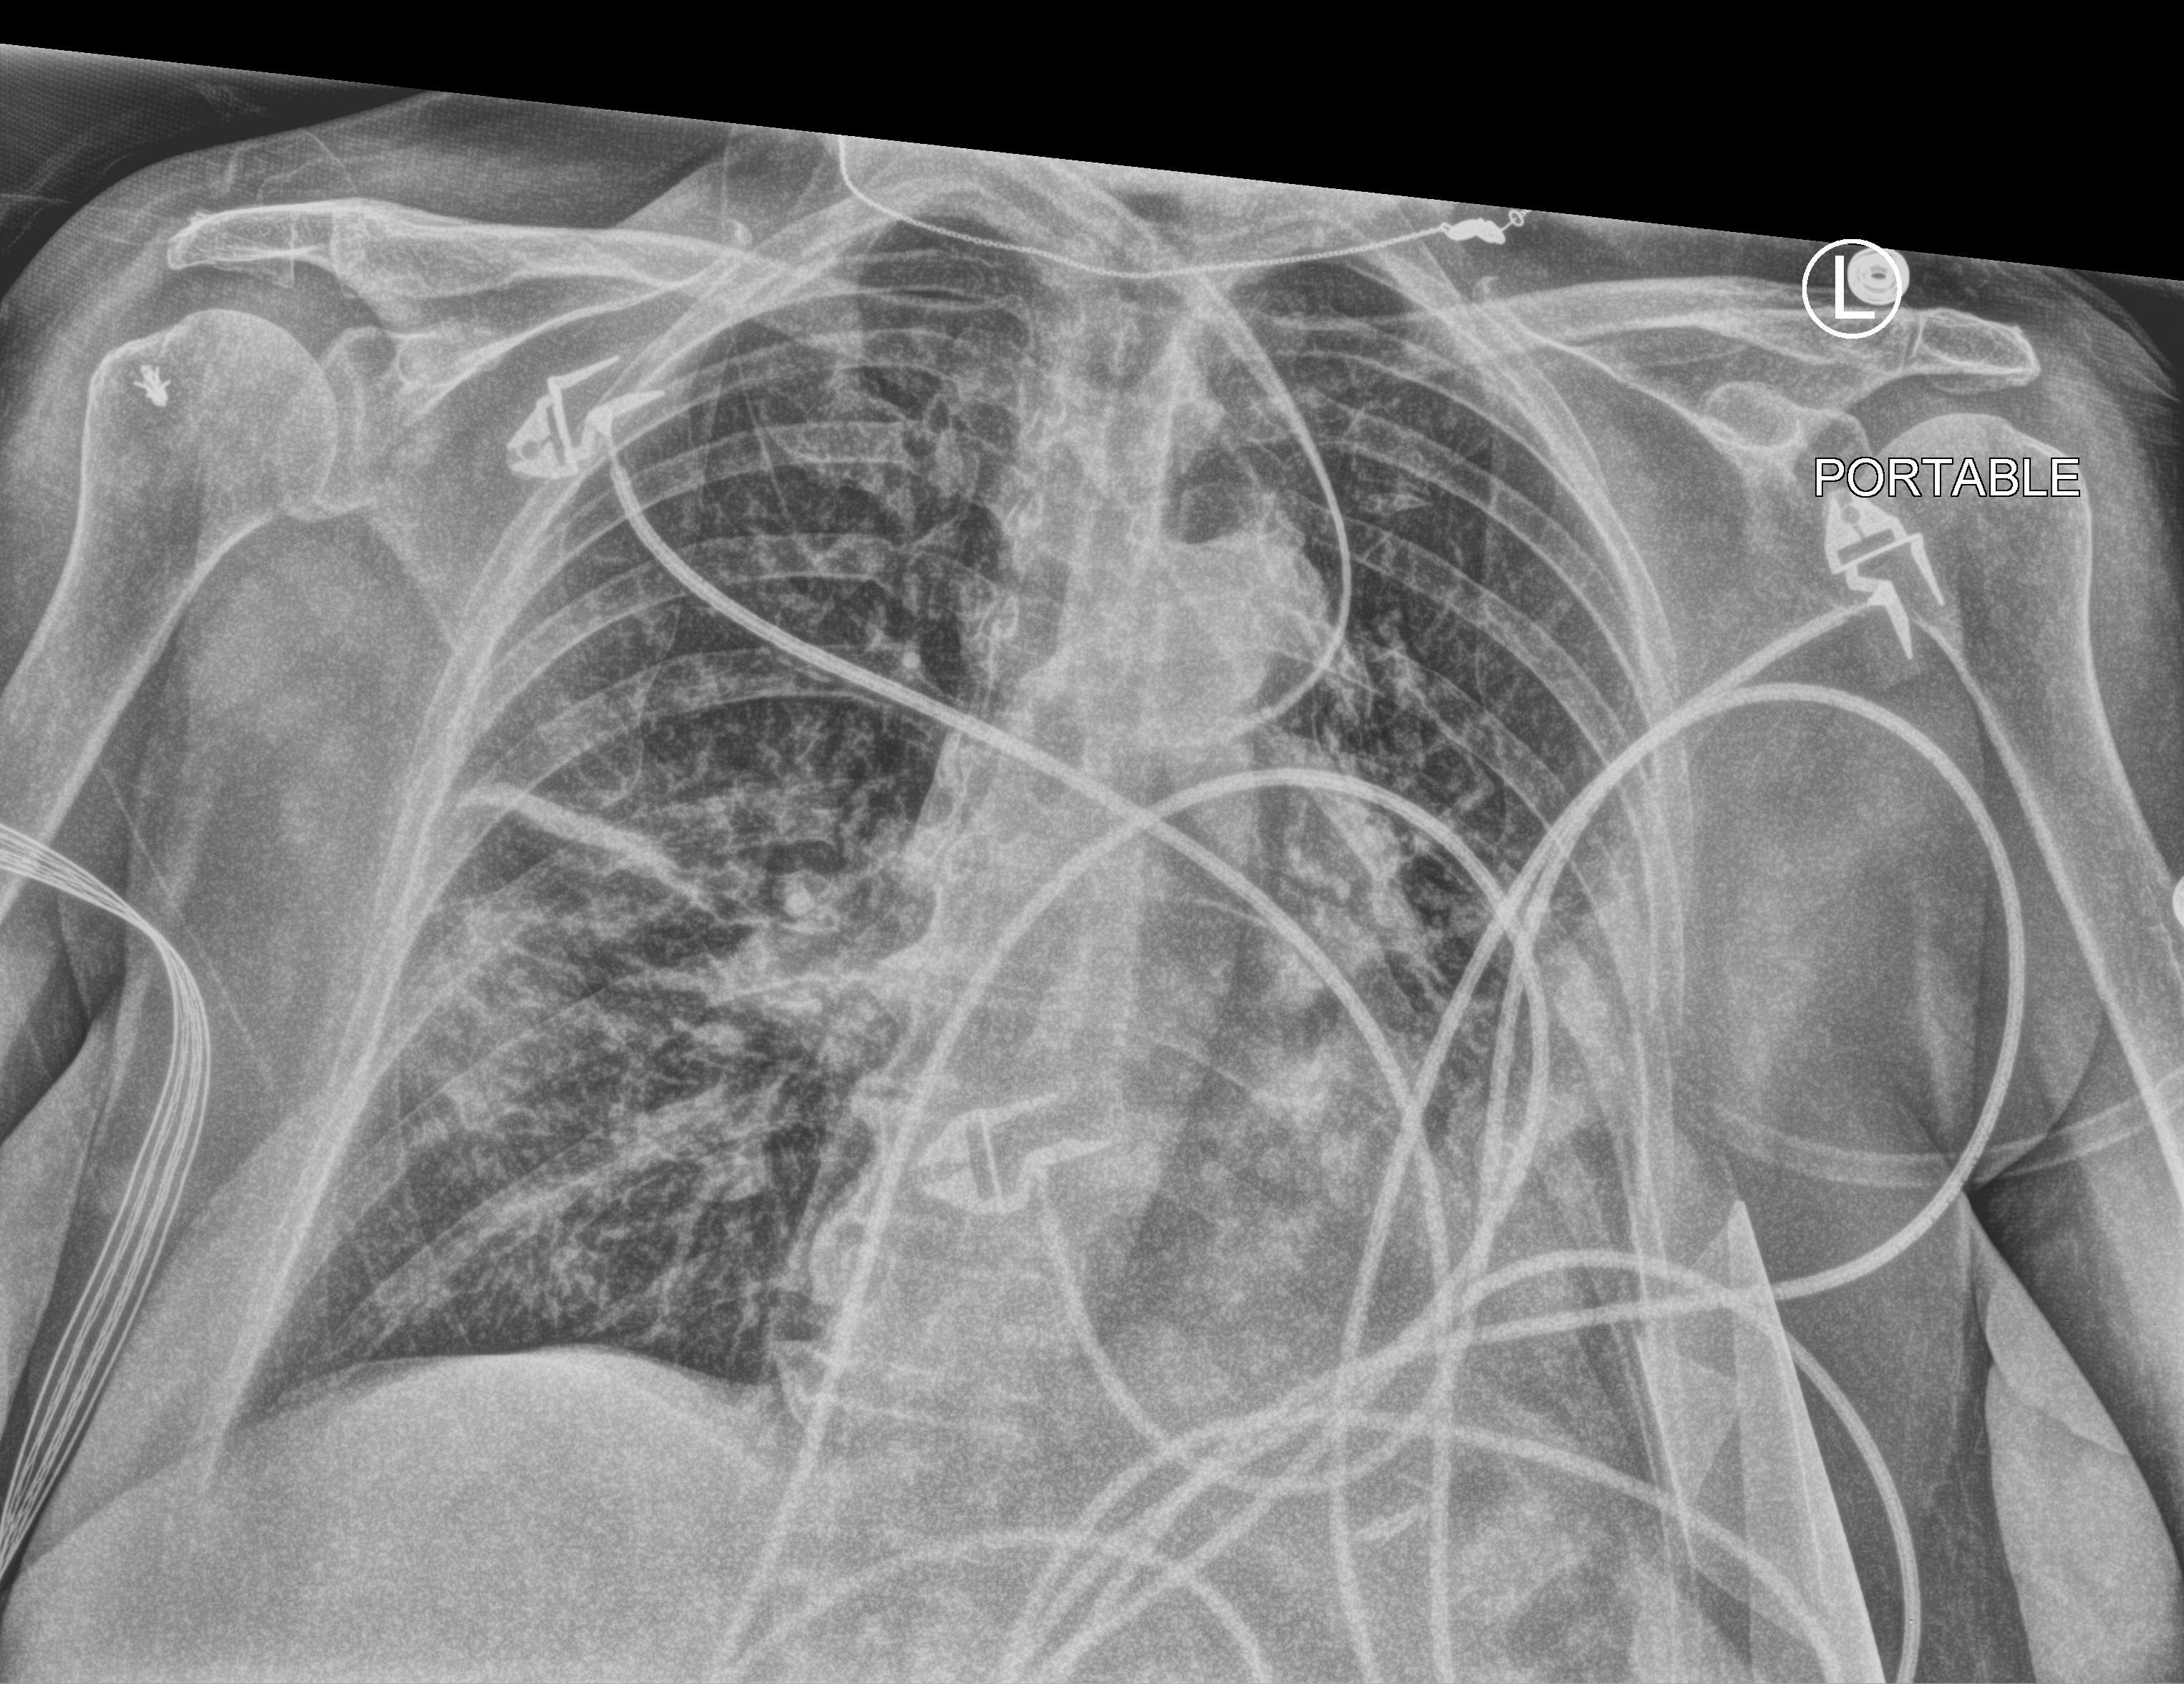
Bedside chest radiograph (computed radiography). Female patient hospitalised with COVID-19, age 60–74 years.
Hospital-stay facts (about this admission, not read from this image; timing relative to this image not recorded):
- mechanically ventilated during this hospital stay: no
- length of hospital stay: 8 days
- admitted to intensive care during this hospital stay: no